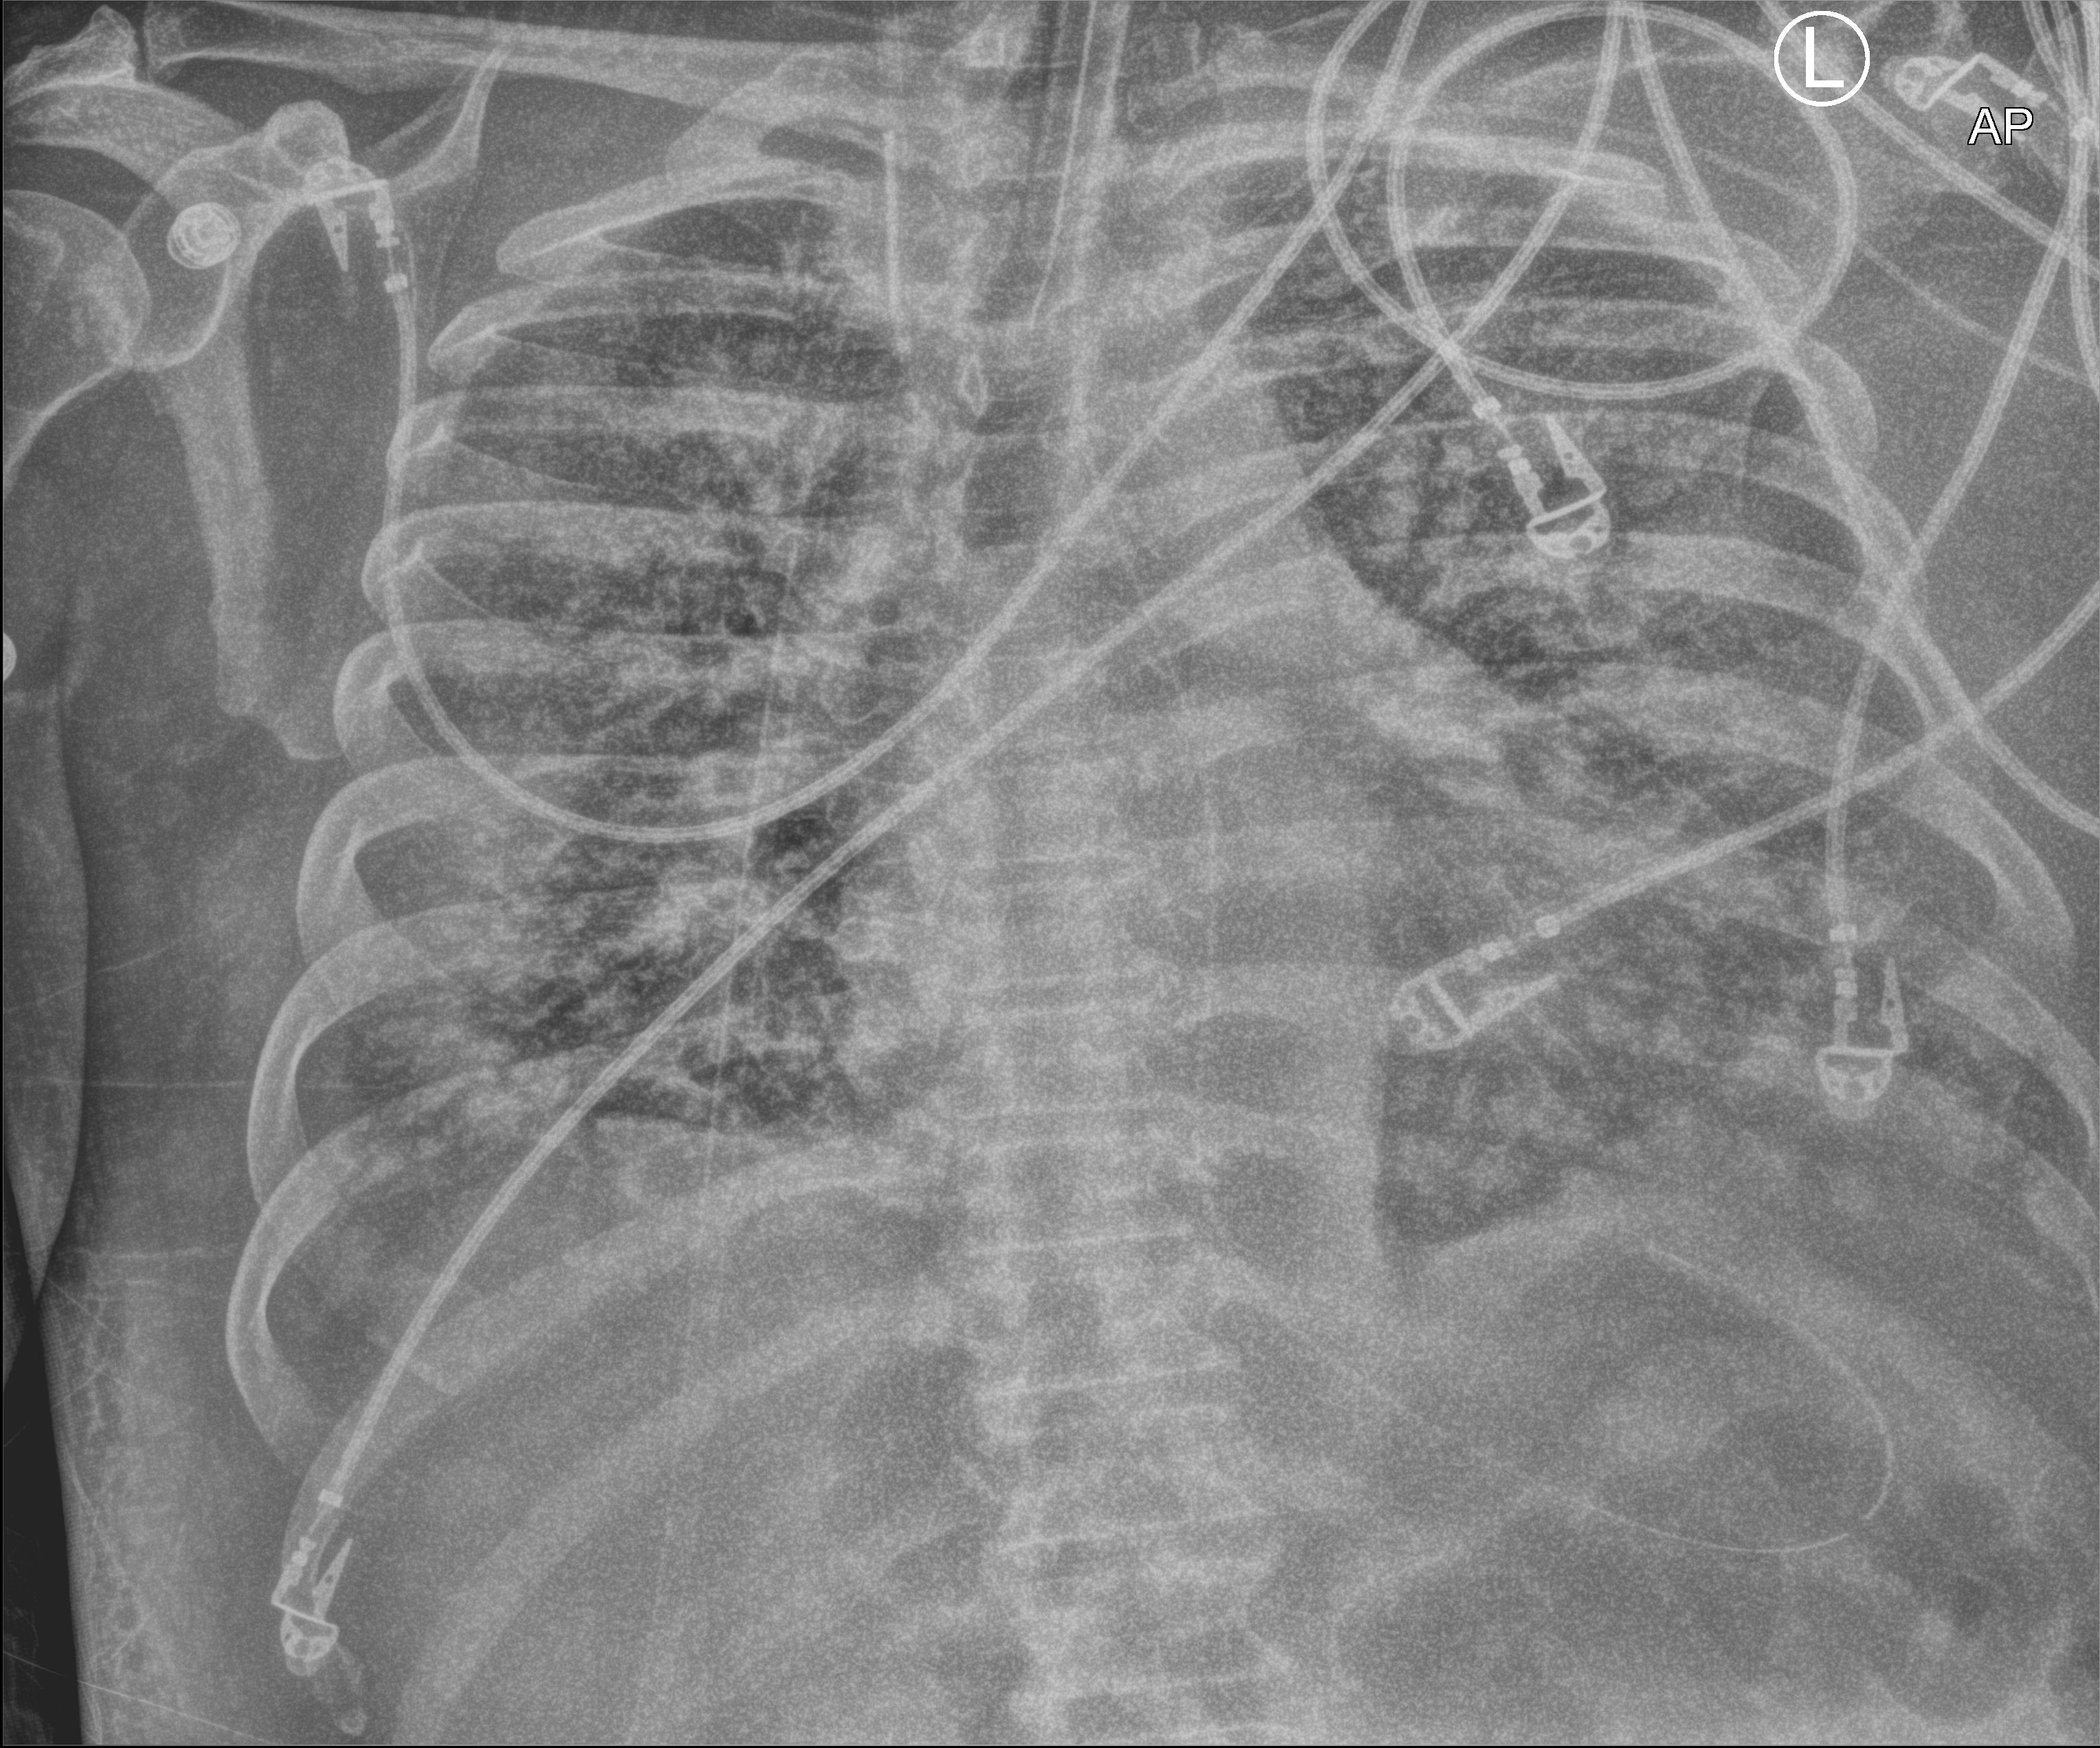
Portable chest radiograph. Patient hospitalised with COVID-19; male, aged 60–74 years.
Admission-level facts for this patient (not findings on this image; timing relative to this image not recorded): admitted to intensive care during this hospital stay: yes; length of hospital stay: 28 days; diabetes (admission record): no.